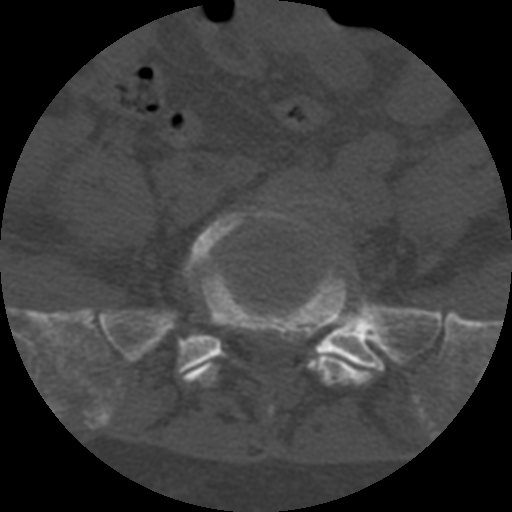
CT including the spine, one axial slice; slice 175 of 708 in the series (ordered by position); reconstruction kernel STANDARD; one of 3 acquisitions stored at this slice position; bone window (W 1800 / L 400 HU); 1.25 mm slice thickness; 512 × 512 image matrix. Patient age 55 years. Case-level facts recorded for this patient, not image findings: primary cancer: colon; vertebrae with lytic lesions (as recorded): T12, L1, L5.
Outlined on this slice (semi-automatic segmentation, software-assisted and operator-edited):
- L5 vertebra: bounding box [x1, y1, x2, y2] px = [184, 210, 374, 416]